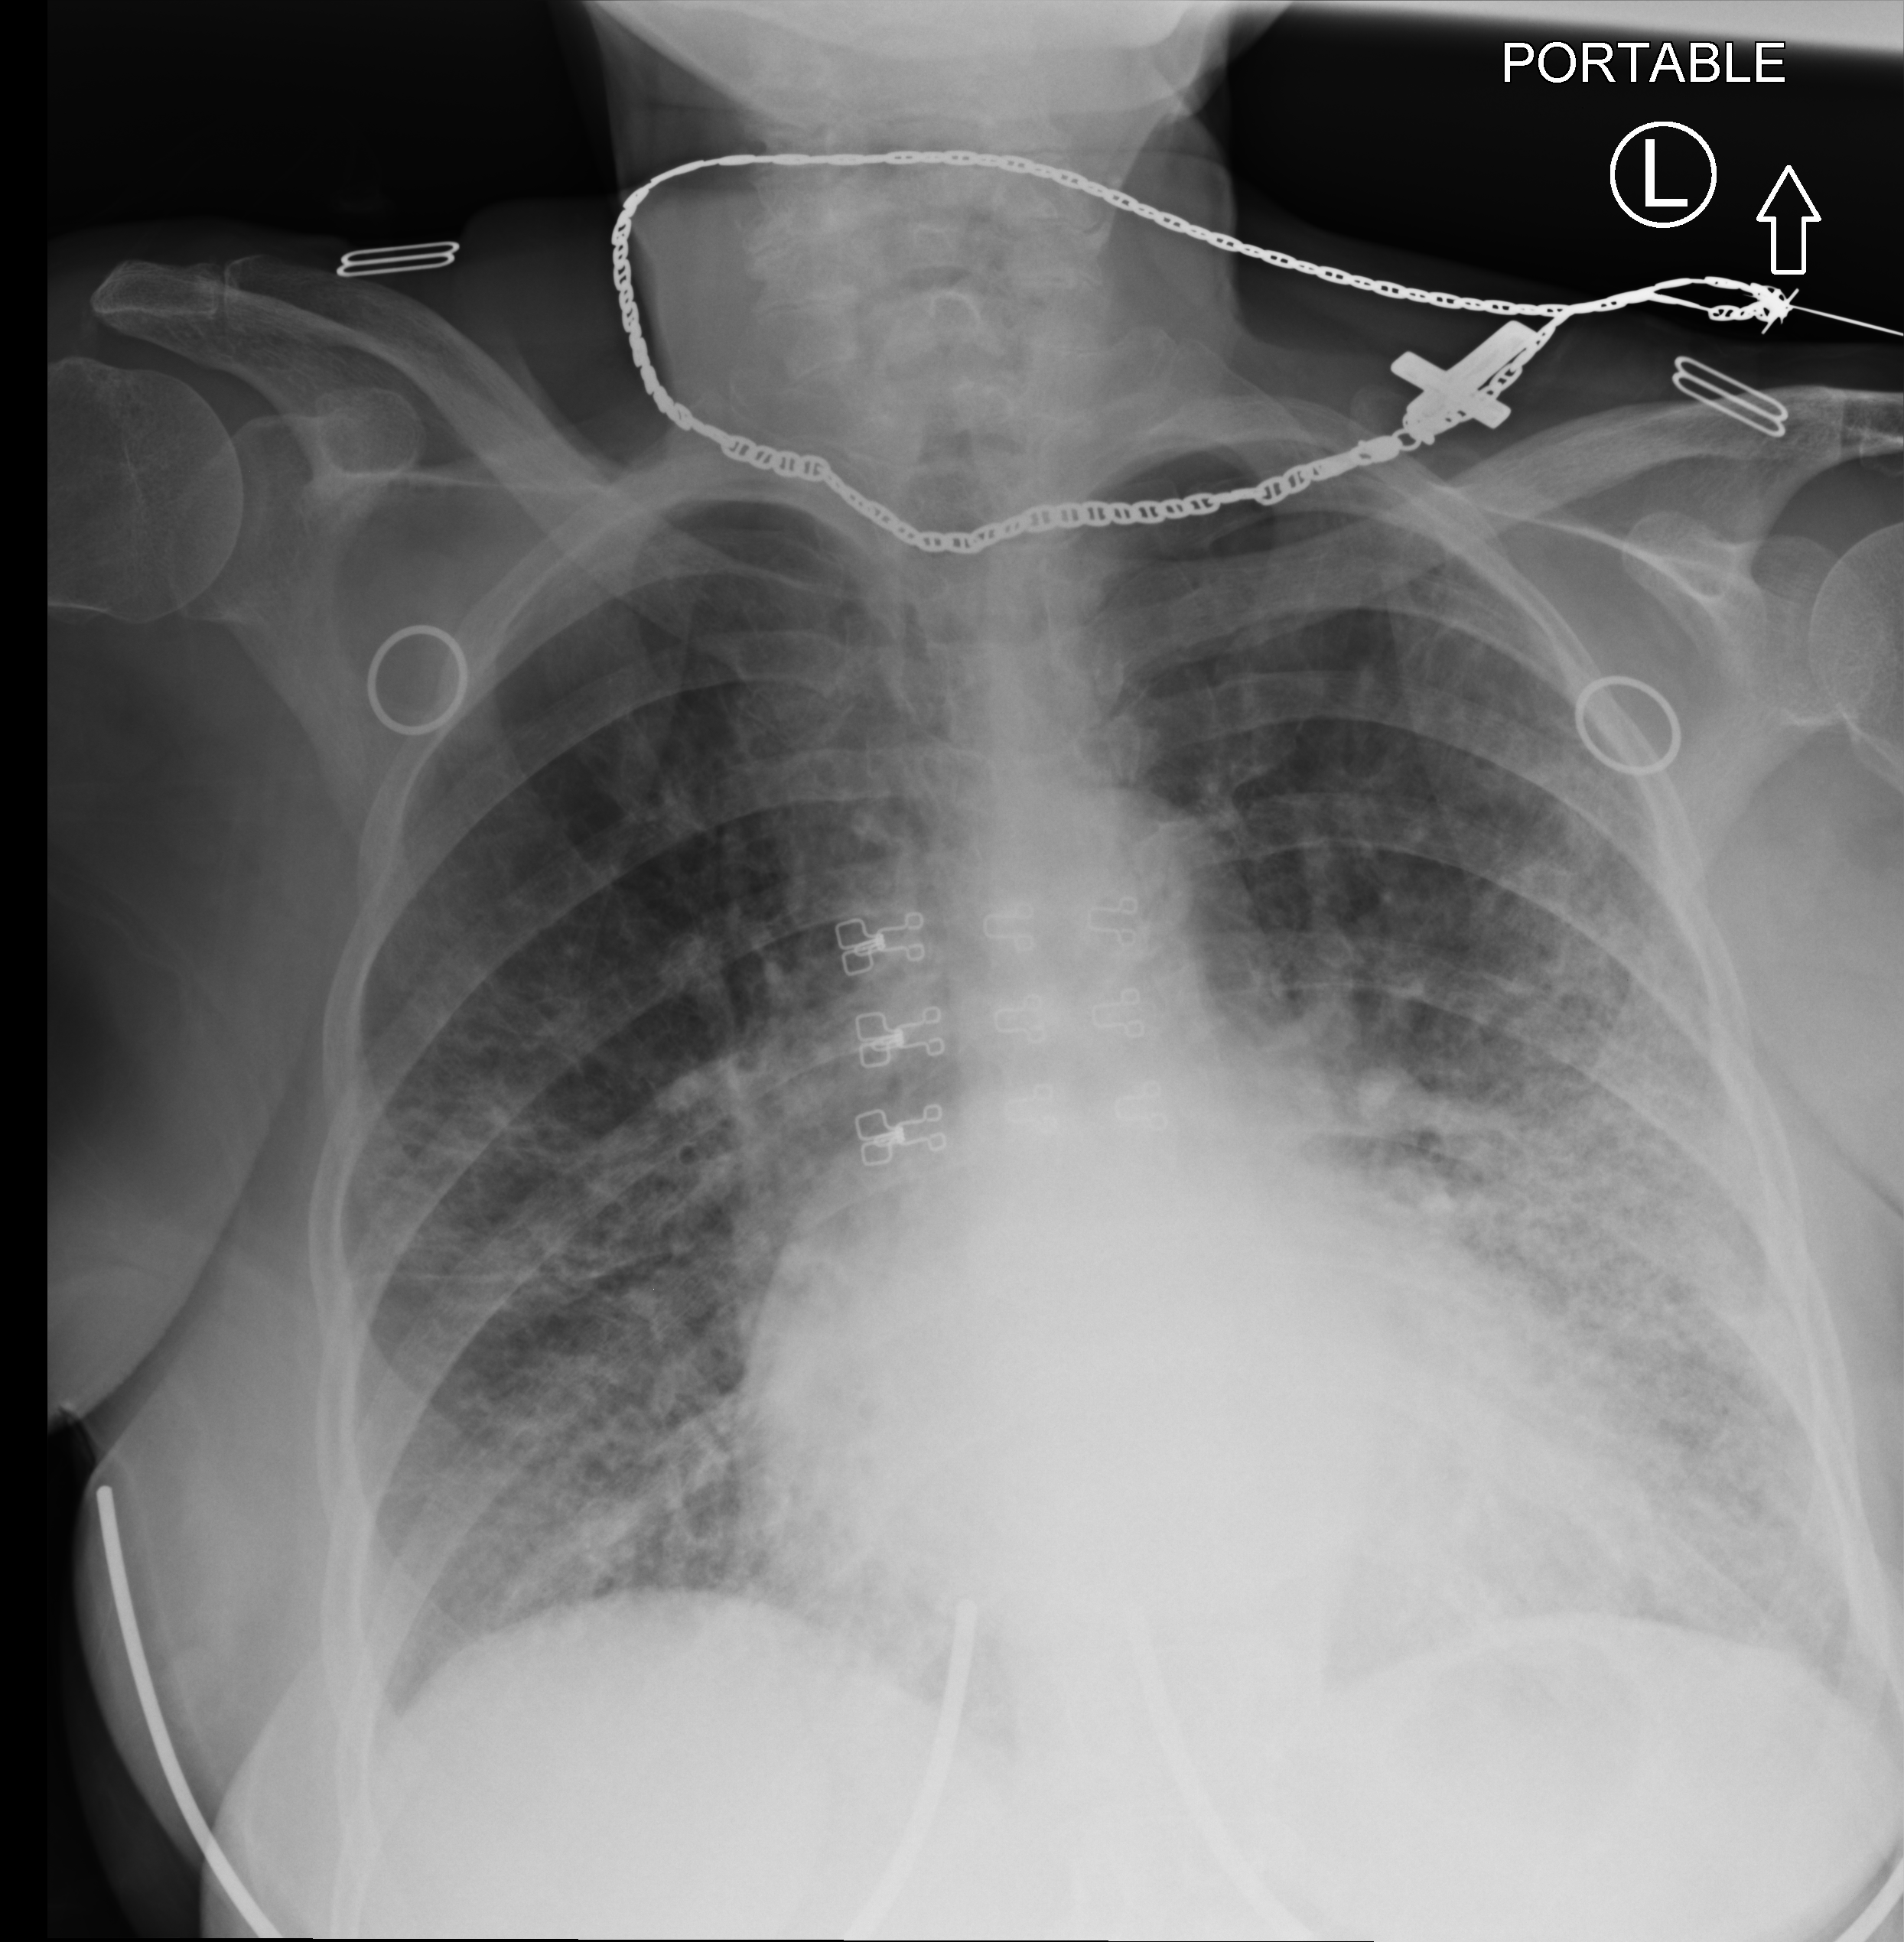
Chest X-ray (portable). Patient hospitalised with COVID-19; female, aged 75–90 years.
Admission-level facts for this patient (not findings on this image; timing relative to this image not recorded): smoking status (admission record): never; admitted to intensive care during this hospital stay: no.